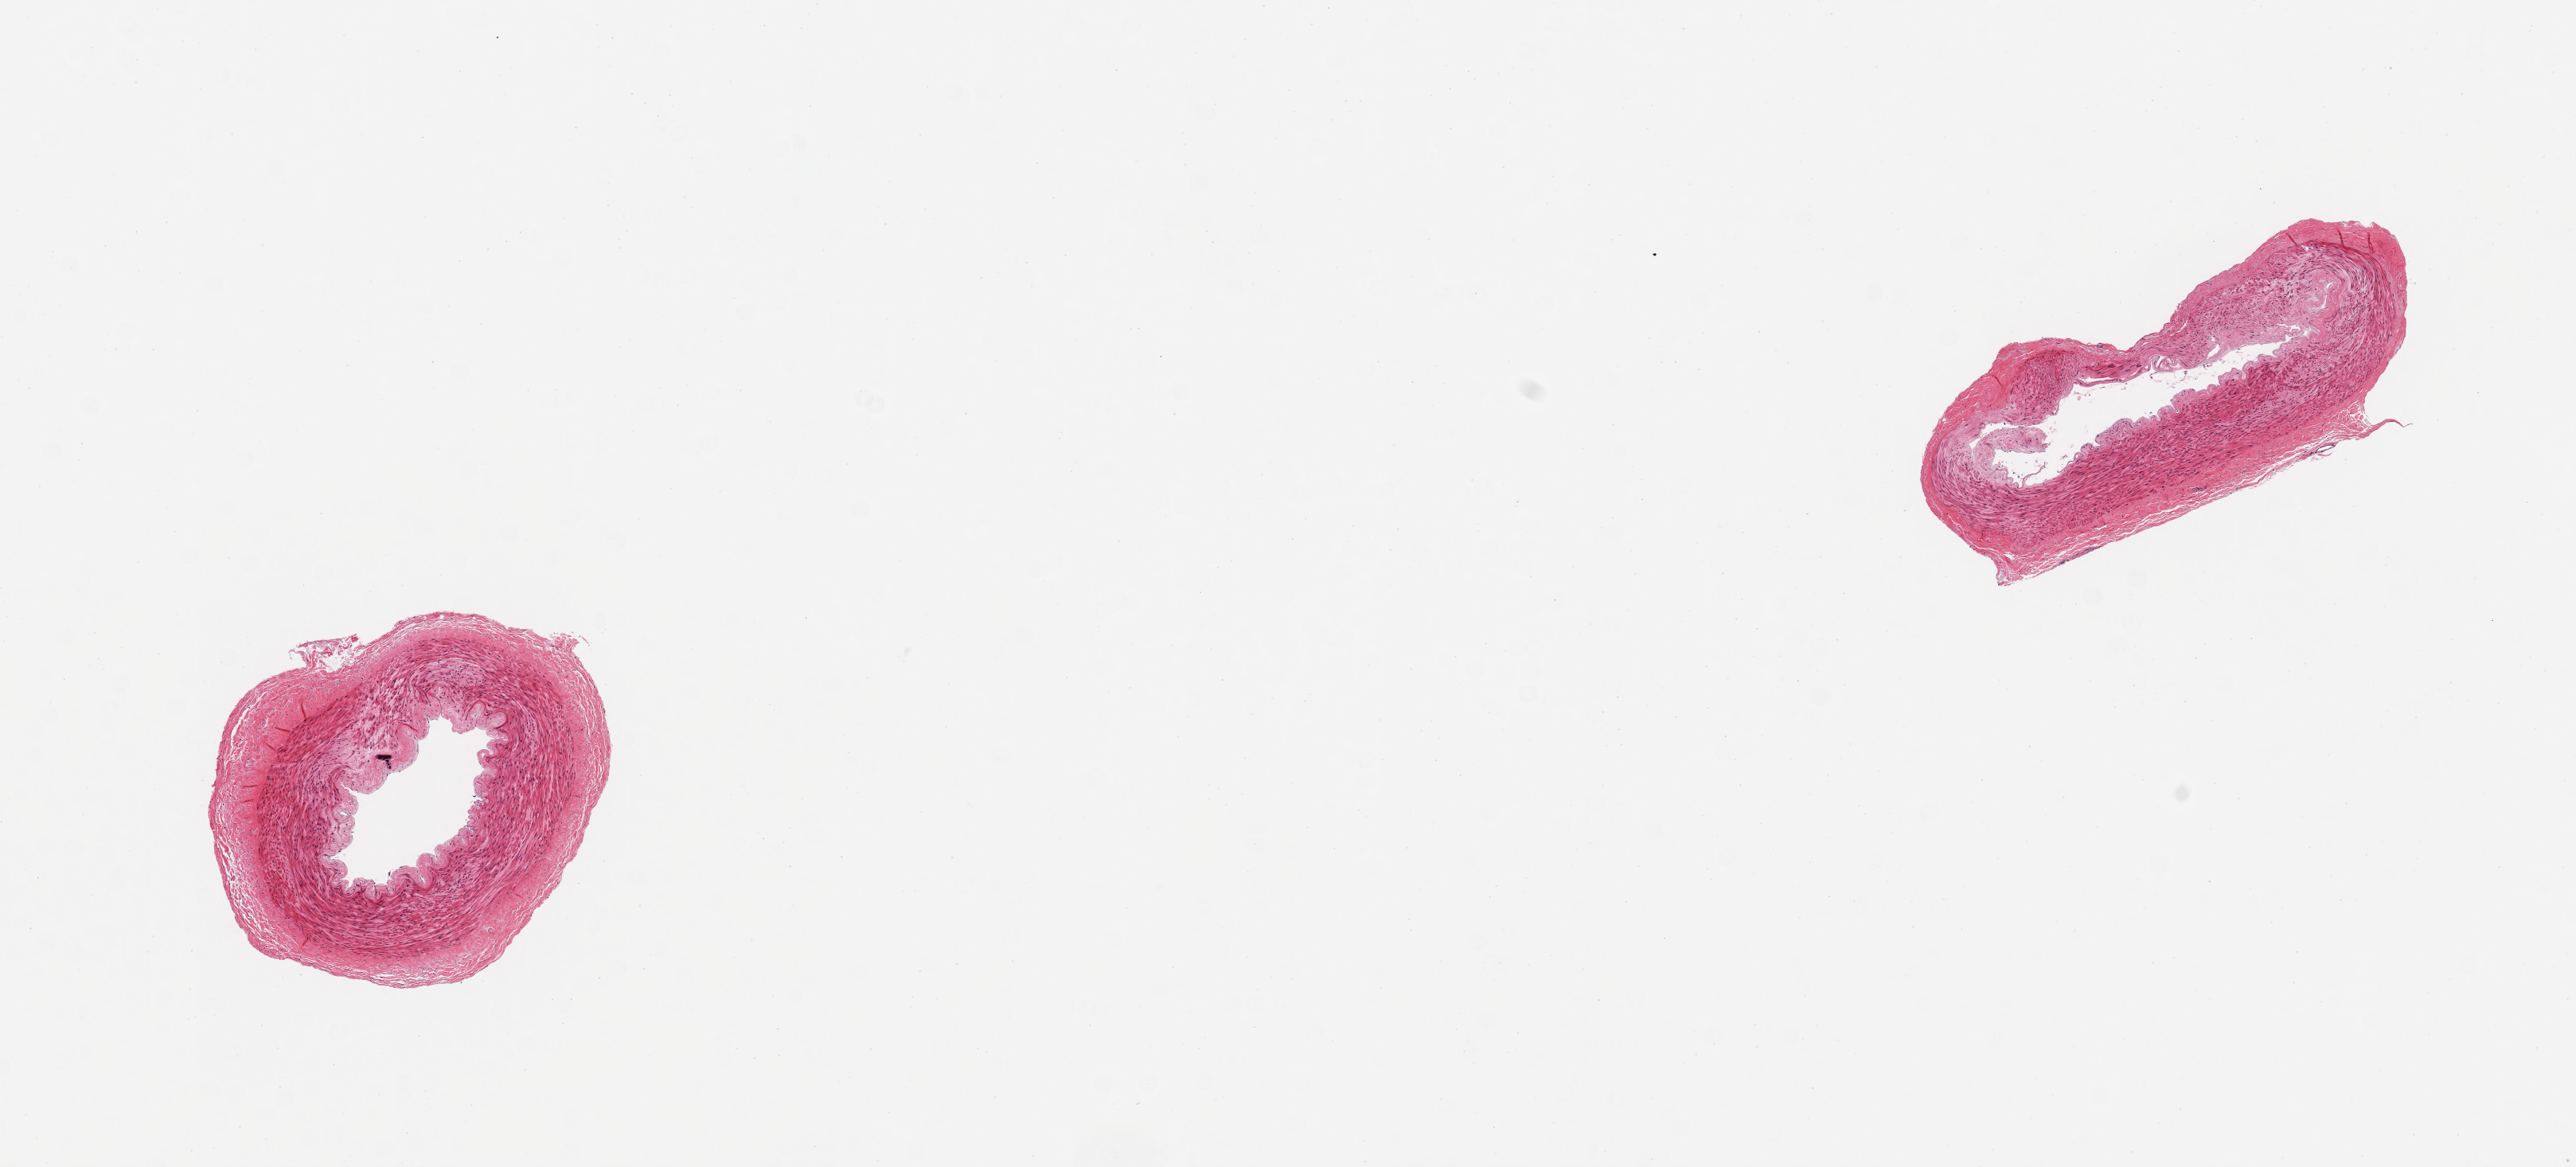
Whole-slide image, haematoxylin and eosin stain, low-resolution overview of the scanned area, about 12.8 x 5.8 mm, PAXgene-fixed, paraffin-embedded tissue, section of tibial artery (target tissue), donor tissue sample.
Reviewer comment on this tissue sample: 2 pieces; well trimmed; minimal plaque; small calcific focus.